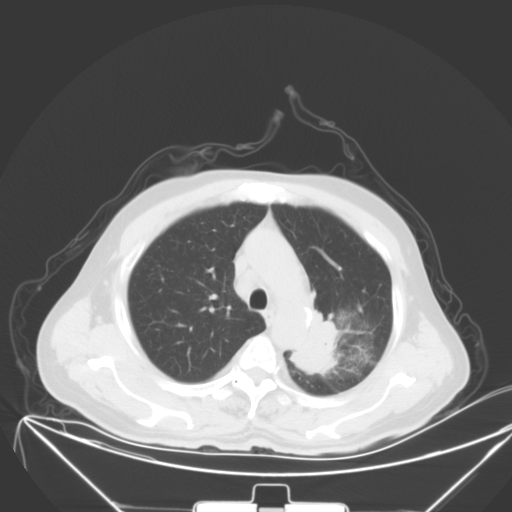
Chest CT, one axial slice; position 44 of 64 along the scan axis; 120 kVp; lung window (W 1500 / L -600 HU); 512 × 512 image matrix, field of view 431 × 431 mm. Patient: male, 58 years. From the clinical record (not read from this slice): clinical TNM (as recorded): T2b N3 M1b; histopathological grade: G3.
Outlined on this slice (bounding box drawn by a radiologist):
- lung tumour (recorded histology: adenocarcinoma): bounding box (x1, y1, x2, y2) in pixels: (292, 301, 338, 379)